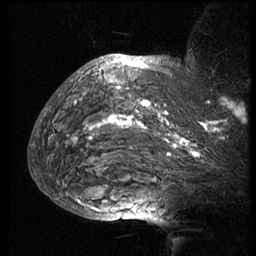
Breast MRI (dynamic contrast-enhanced), one sagittal slice; slice 54 of 74 in the series (ordered by position); 3 images stored at this slice position (order not interpretable as contrast timing); 1.5 T; TE 4.2 ms, TR 8.9 ms; 256 × 256 image matrix, field of view 200 × 200 mm. Female patient, age 57 years. Case-level facts recorded for this patient, not image findings: setting: breast cancer imaged before/during neoadjuvant chemotherapy; receptor status: HER2-positive.
Structures marked on this image (semi-automatically segmented with operator editing):
- analysis volume of interest (the breast-tissue region the enhancement analysis was run in; not a lesion): bounding box <51,67,248,173> (left, top, right, bottom; pixels)
- tumour enhancement mask (voxels above the 140 % enhancement threshold inside the analysis volume of interest): <76,67,245,157>